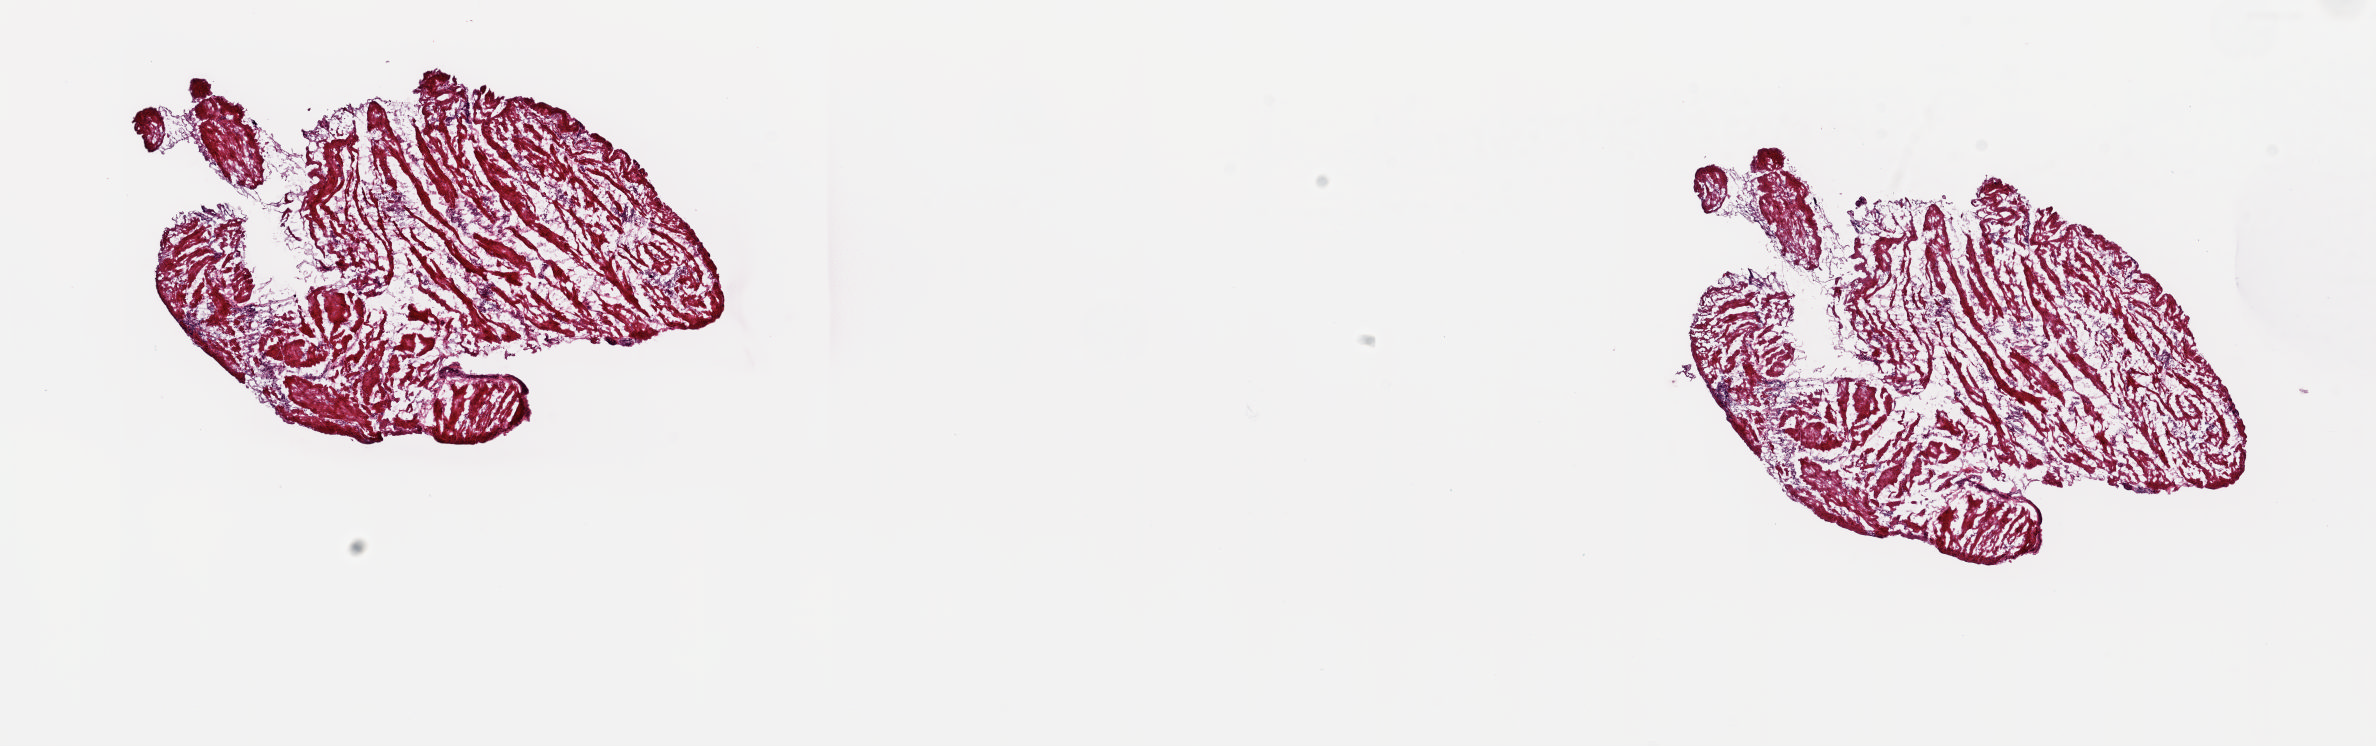
H&E-stained whole-slide image, a low-resolution overview of the entire scanned area, about 18.8 x 5.9 mm (acquisition: 20x scan); frozen section from the top of the tissue portion; esophagus, solid tissue normal (non-tumour tissue) sample. Female patient; age at initial diagnosis 51 years. Composition of this section per pathologist review: tumour cells 0%, tumour nuclei 0%, normal cells 100%, stromal cells 0%, necrosis 0%. Inflammatory infiltration, as recorded: lymphocyte infiltration 1%, monocyte infiltration 1%, neutrophil infiltration 3%.
This section: solid tissue normal sample (biorepository sample class). Patient diagnosis: Squamous cell carcinoma, keratinizing, NOS.